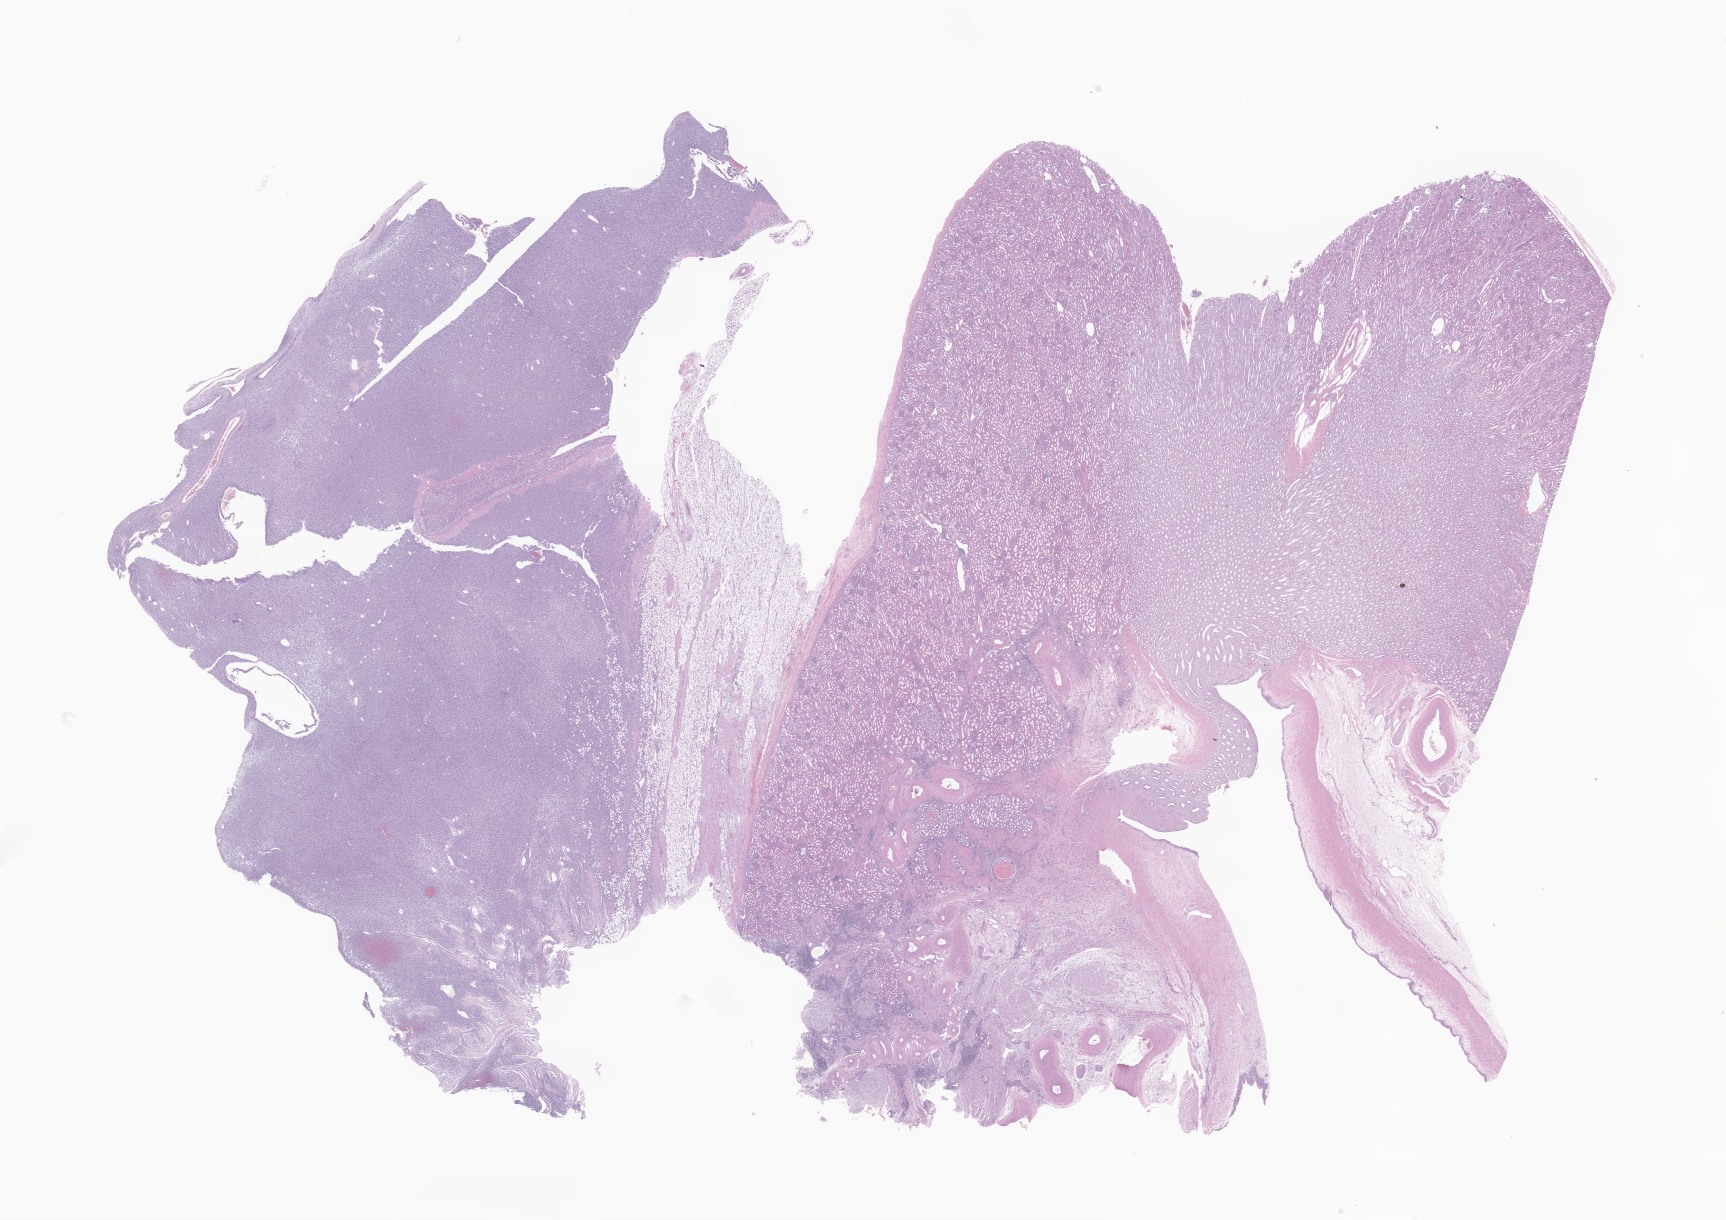
Hematoxylin and eosin (H&E) whole-slide image of tumor tissue from the kidney, a low-resolution overview of the entire scanned area, about 29.1 x 20.6 mm, formalin-fixed paraffin-embedded section. Male patient, age 464 days (about 1.3 years).
Diagnosis (ICD-O-3 morphology term): Sarcoma, NOS.